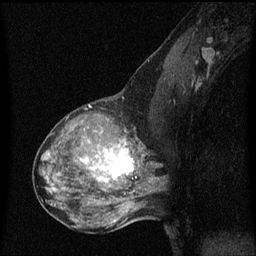
Breast MRI (dynamic contrast-enhanced), one sagittal slice. Slice 35 of 60 in the series (ordered by position). Dynamic contrast-enhanced series, image 2 of 3 at this slice position (ordered by acquisition). 1.5 T. TE 4.2 ms, TR 8 ms. 256 × 256 image matrix, field of view 200 × 200 mm. Patient: female, 50 years.
Annotated regions visible in this slice (semi-automatic segmentation, software-assisted and operator-edited):
- analysis volume of interest (the breast-tissue region the enhancement analysis was run in; not a lesion): bounding box [x1, y1, x2, y2] px = [91, 126, 141, 189]
- tumour enhancement mask (voxels above the 70 % enhancement threshold inside the analysis volume of interest): [96, 142, 134, 183]